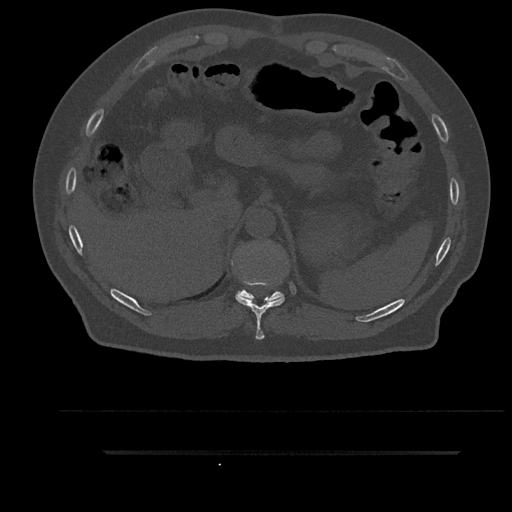
CT including the spine, one axial slice. Position 339 of 797 along the scan axis. 120 kVp. Bone window (W 1800 / L 400 HU). 0.5 mm slice thickness. 512 × 512 image matrix. Patient: male, 63 years. From the clinical record (not read from this slice): primary cancer: renal.
Structures marked on this image (semi-automatically segmented with operator editing):
- T10 vertebra: bounding box <232,260,285,340> (left, top, right, bottom; pixels)
- T11 vertebra: <236,249,284,303>